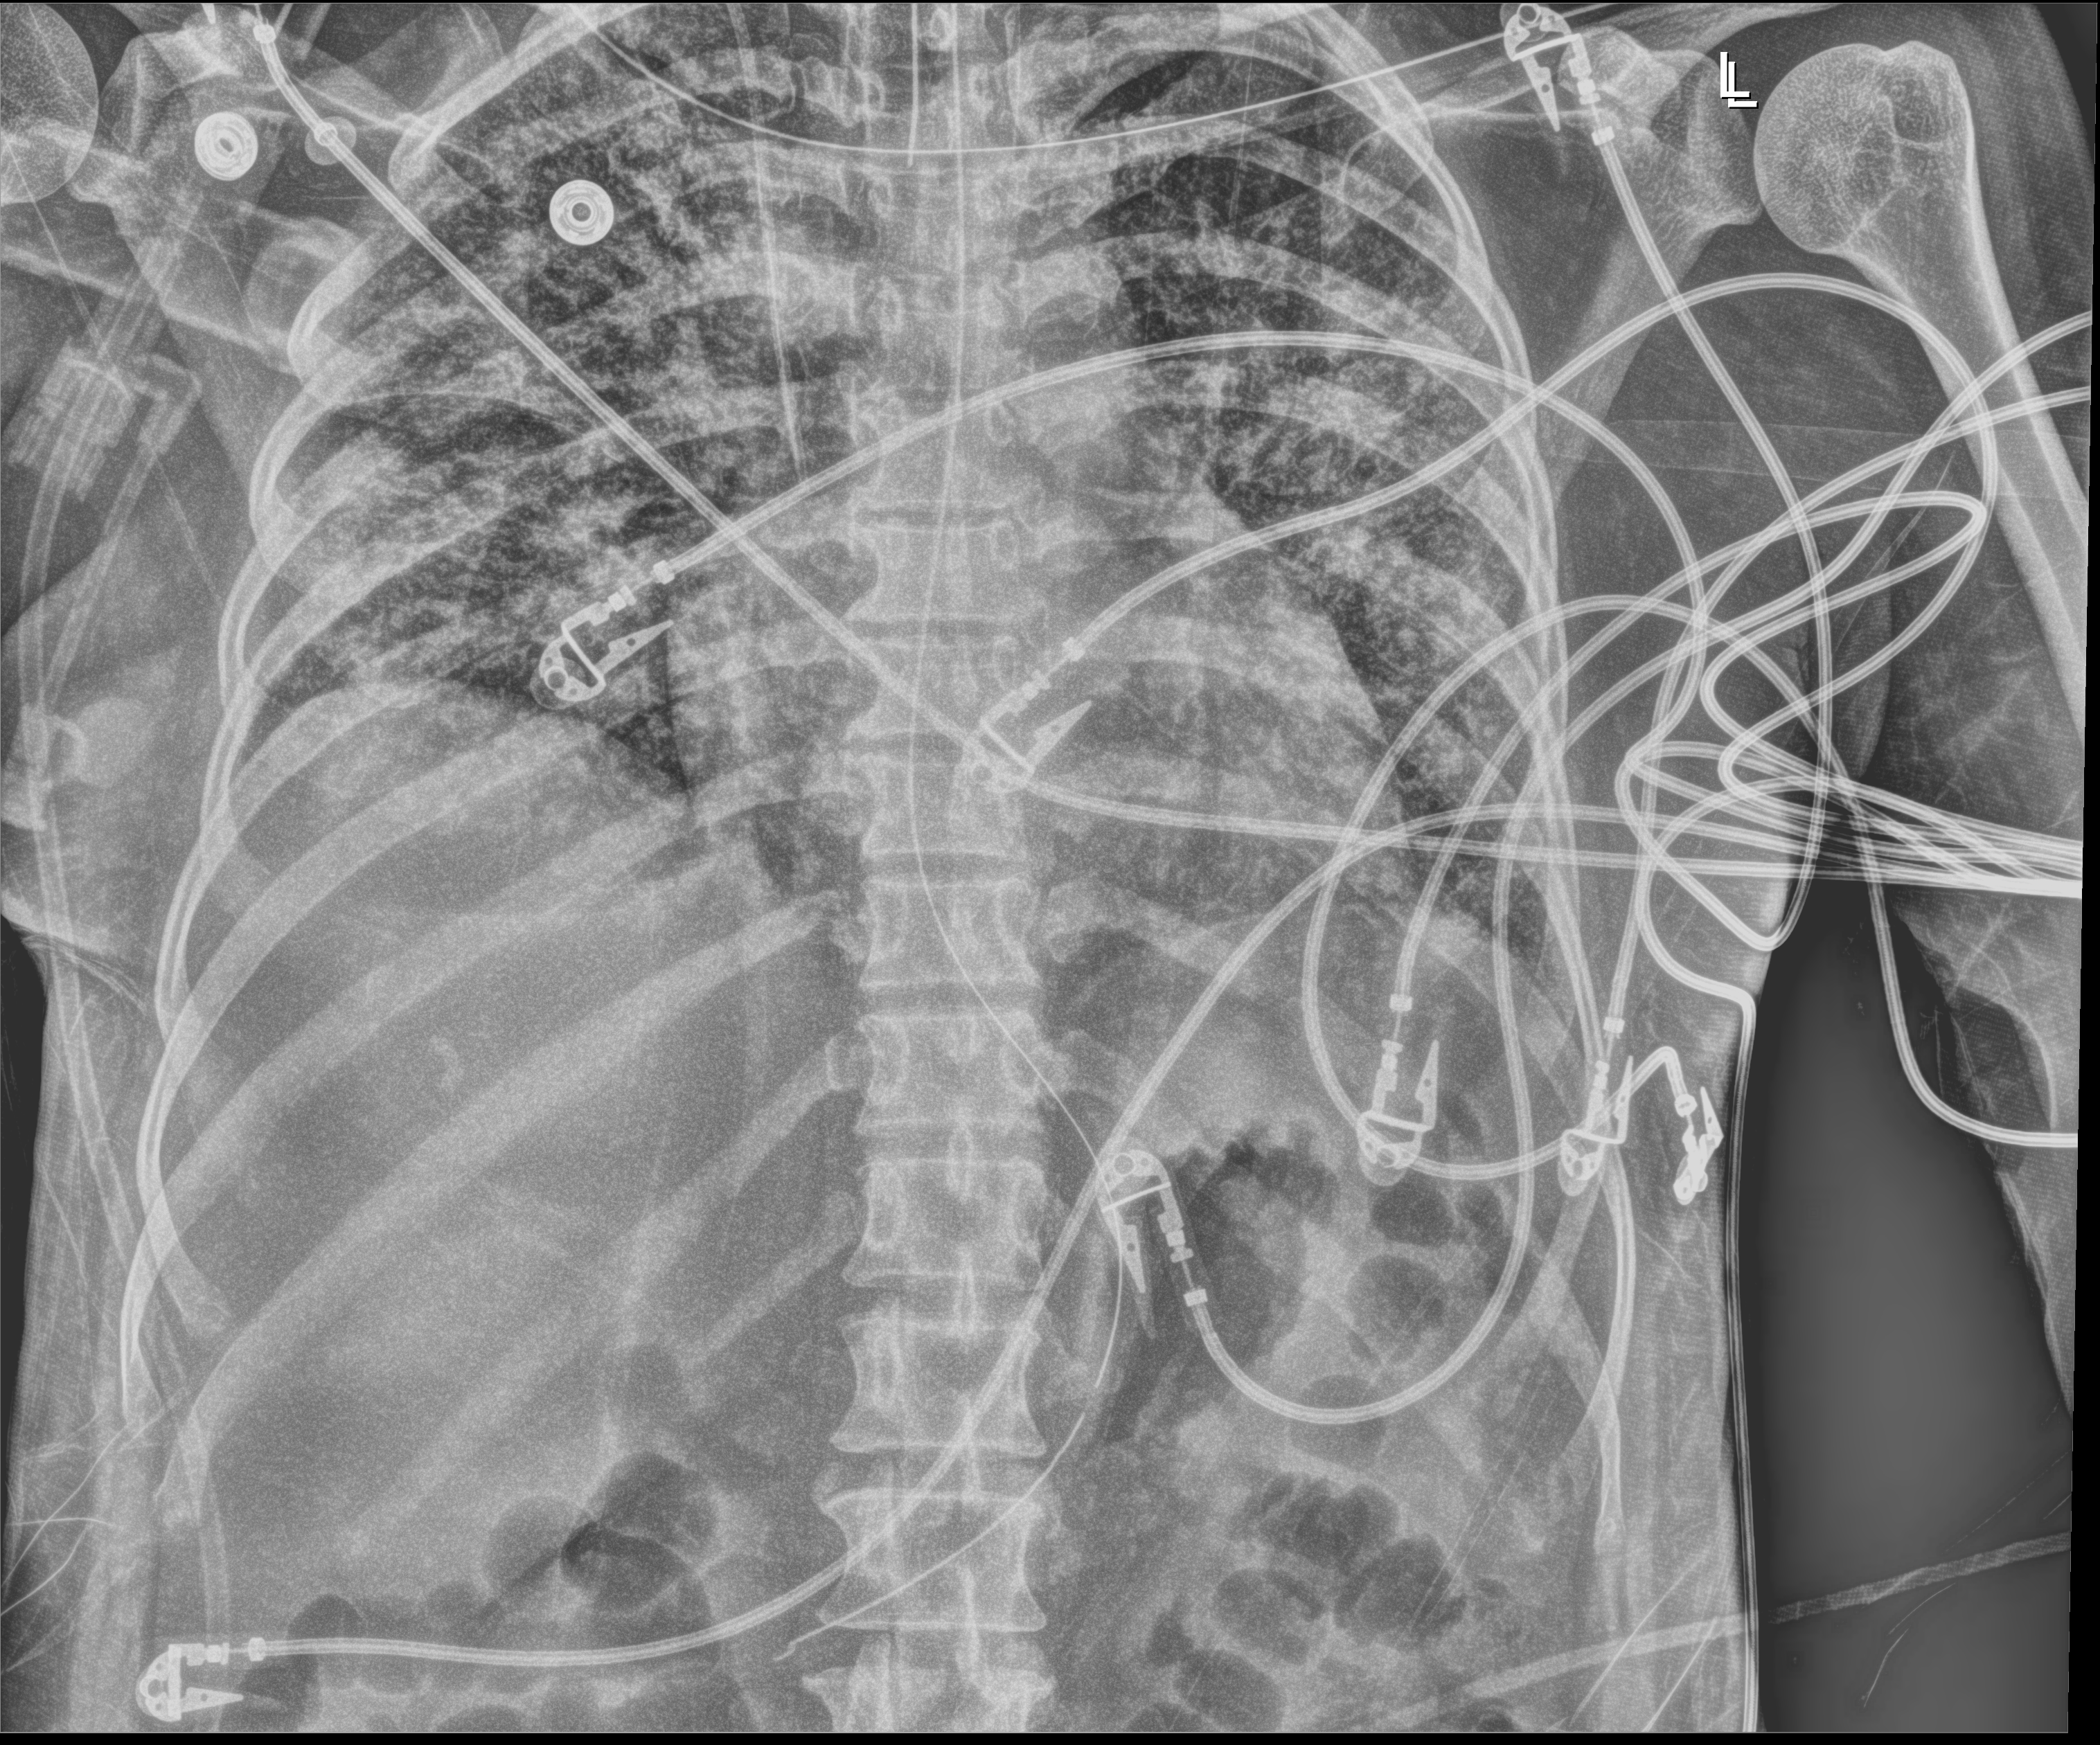
Portable chest radiograph. Female patient hospitalised with COVID-19, age 18–59 years.
Hospital-stay facts (about this admission, not read from this image; timing relative to this image not recorded): other chronic lung disease (admission record): no; length of hospital stay: 71 days; diabetes (admission record): no.